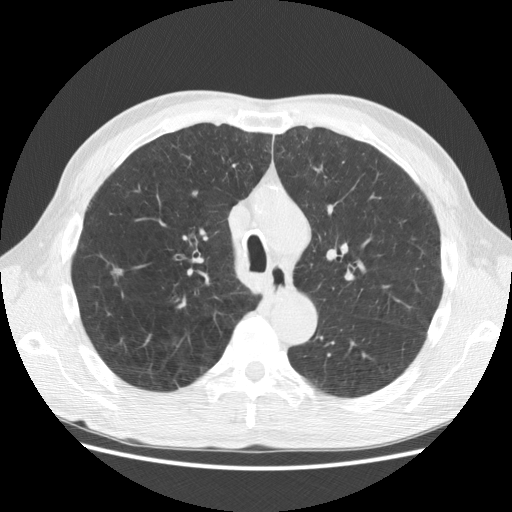
Chest CT (low-dose screening protocol), one axial image; baseline annual screen; lung window (W 1500 / L -600 HU); 2.5 mm slice thickness; standard (soft-tissue) reconstruction kernel (STANDARD); 512 × 512 image matrix. Male participant, aged 62 years at enrolment. Current smoker at enrolment.
Expert reader's lesion annotation, bounding box [x1, y1, x2, y2] px = [102, 260, 137, 294]. The screening reader recorded 2 non-calcified nodules or masses ≥4 mm on this exam; which of them this box marks is not recorded. Official screen result: positive, change unspecified: nodule(s) >= 4 mm or enlarging nodule(s), mass(es), or other non-specific abnormalities suspicious for lung cancer.